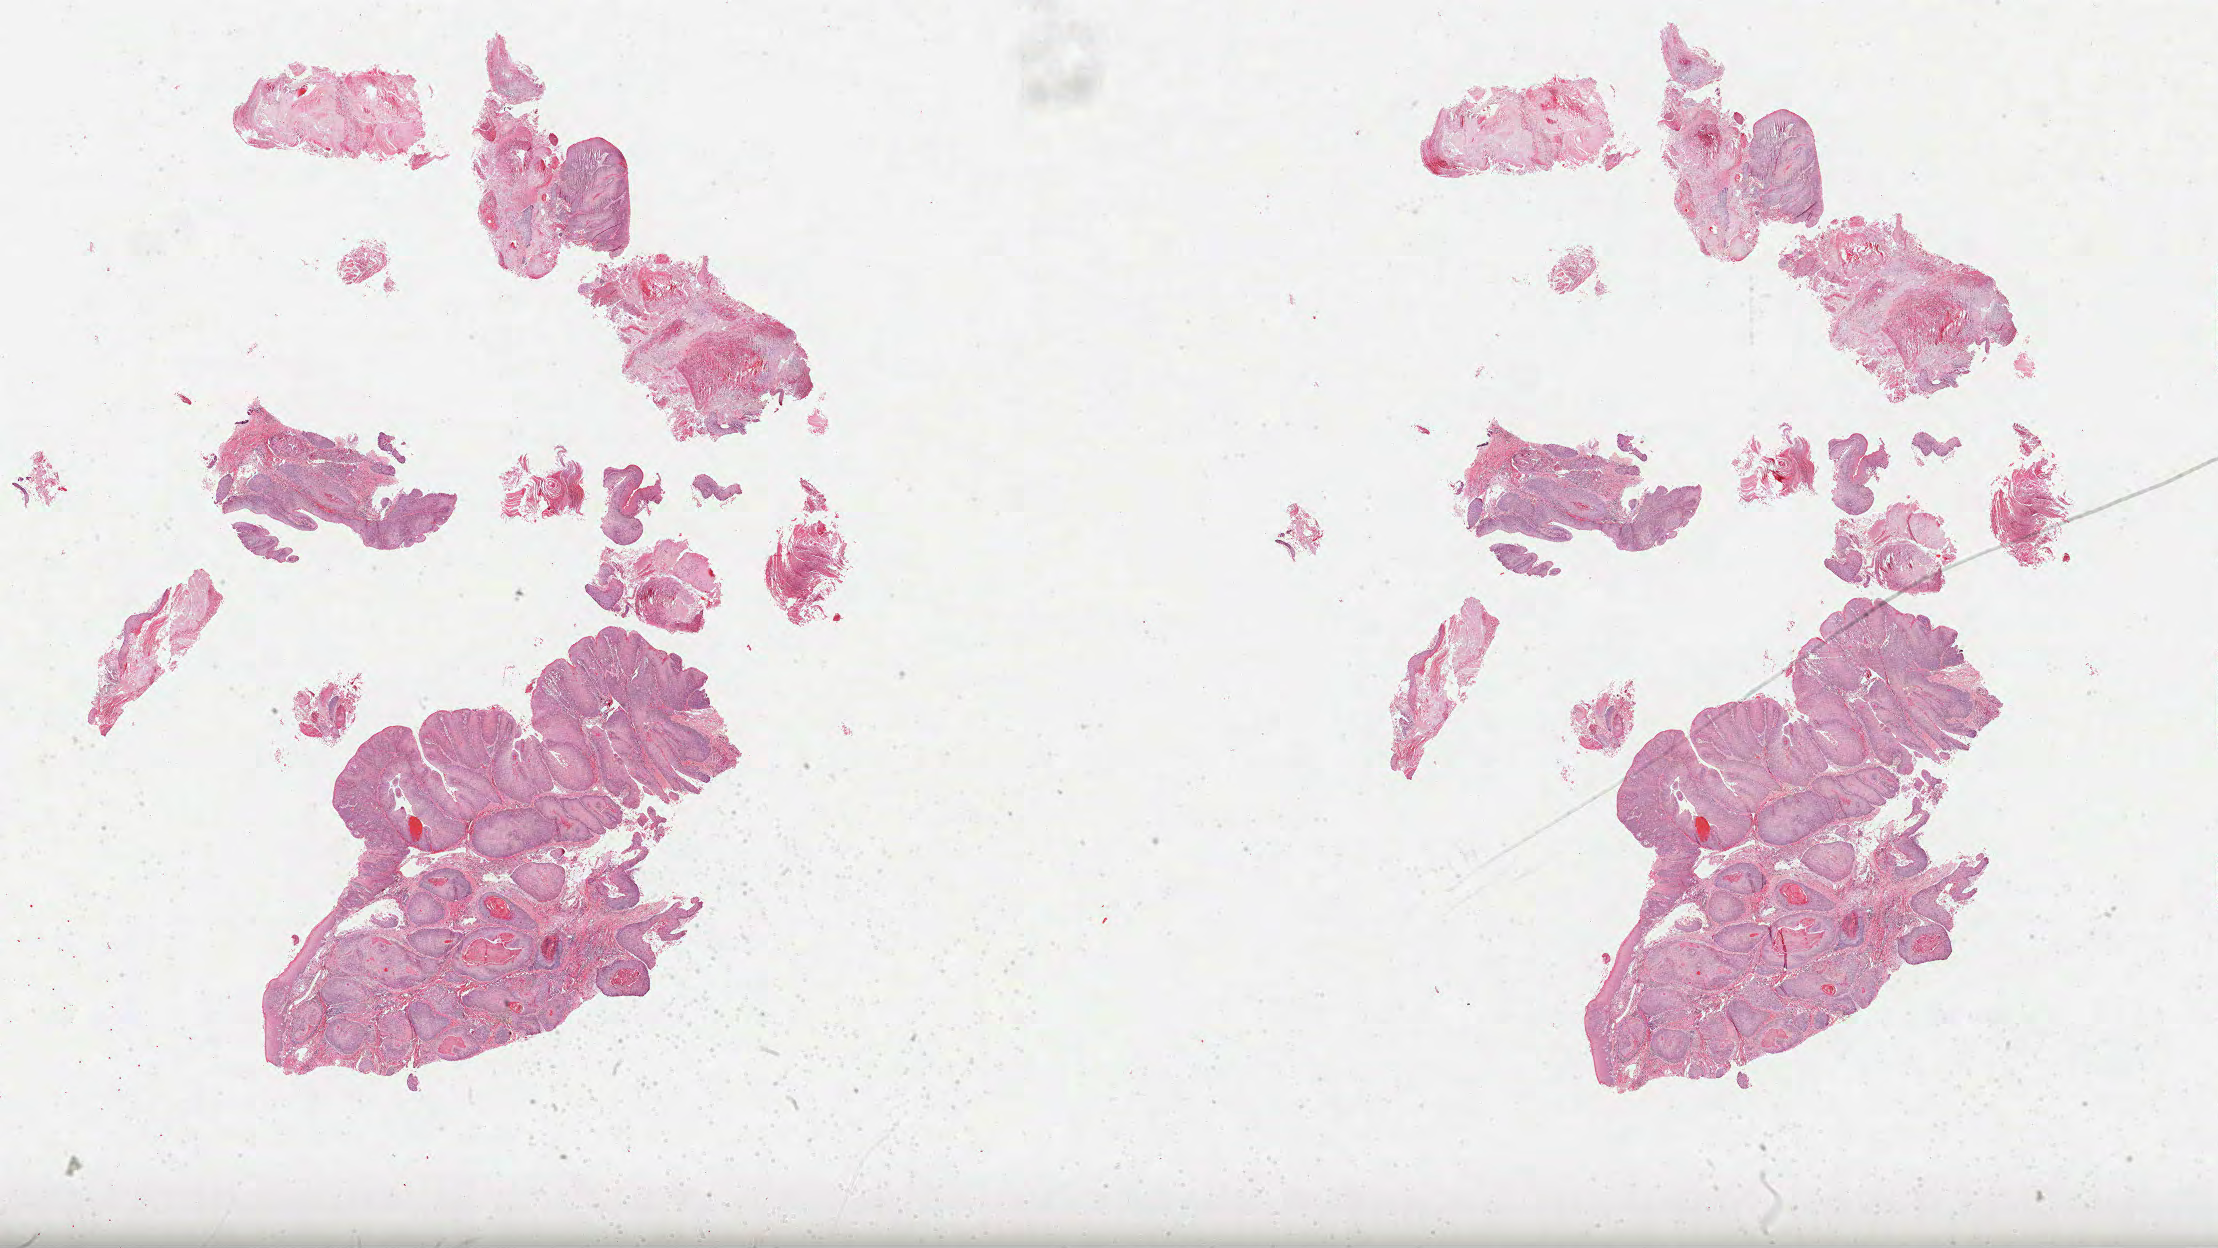
H&E-stained whole-slide image — low-resolution overview of the scanned area, about 35.8 x 20.1 mm (acquisition: 40x scan). Formalin-fixed paraffin-embedded (FFPE) diagnostic section. Head and neck, primary tumour sample. Male, age 75 years at initial diagnosis. Histologic grade: G2 (moderately differentiated).
• AJCC pathologic stage: IVA (6th edition)
• pathologic diagnosis: Squamous cell carcinoma, NOS (gum, NOS)